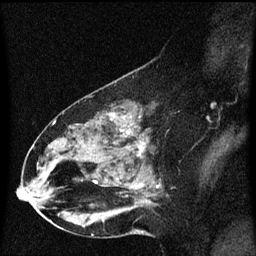
Breast MRI (dynamic contrast-enhanced), one sagittal slice; position 34 of 60 along the scan axis; dynamic contrast-enhanced series, image 2 of 3 at this slice position (ordered by acquisition); 1.5 T; TE 4.2 ms, TR 8.4 ms; 2 mm slice thickness; 256 × 256 image matrix, field of view 200 × 200 mm. Female patient, age 49 years. From the clinical record (not read from this slice): setting: breast cancer imaged before/during neoadjuvant chemotherapy; receptor status: HR-positive, HER2-negative.
Outlined on this slice (semi-automatically segmented with operator editing):
- analysis volume of interest (the breast-tissue region the enhancement analysis was run in; not a lesion): bounding box <27,96,169,221> (left, top, right, bottom; pixels)
- tumour enhancement mask (voxels above the 70 % enhancement threshold inside the analysis volume of interest): <95,132,145,183>